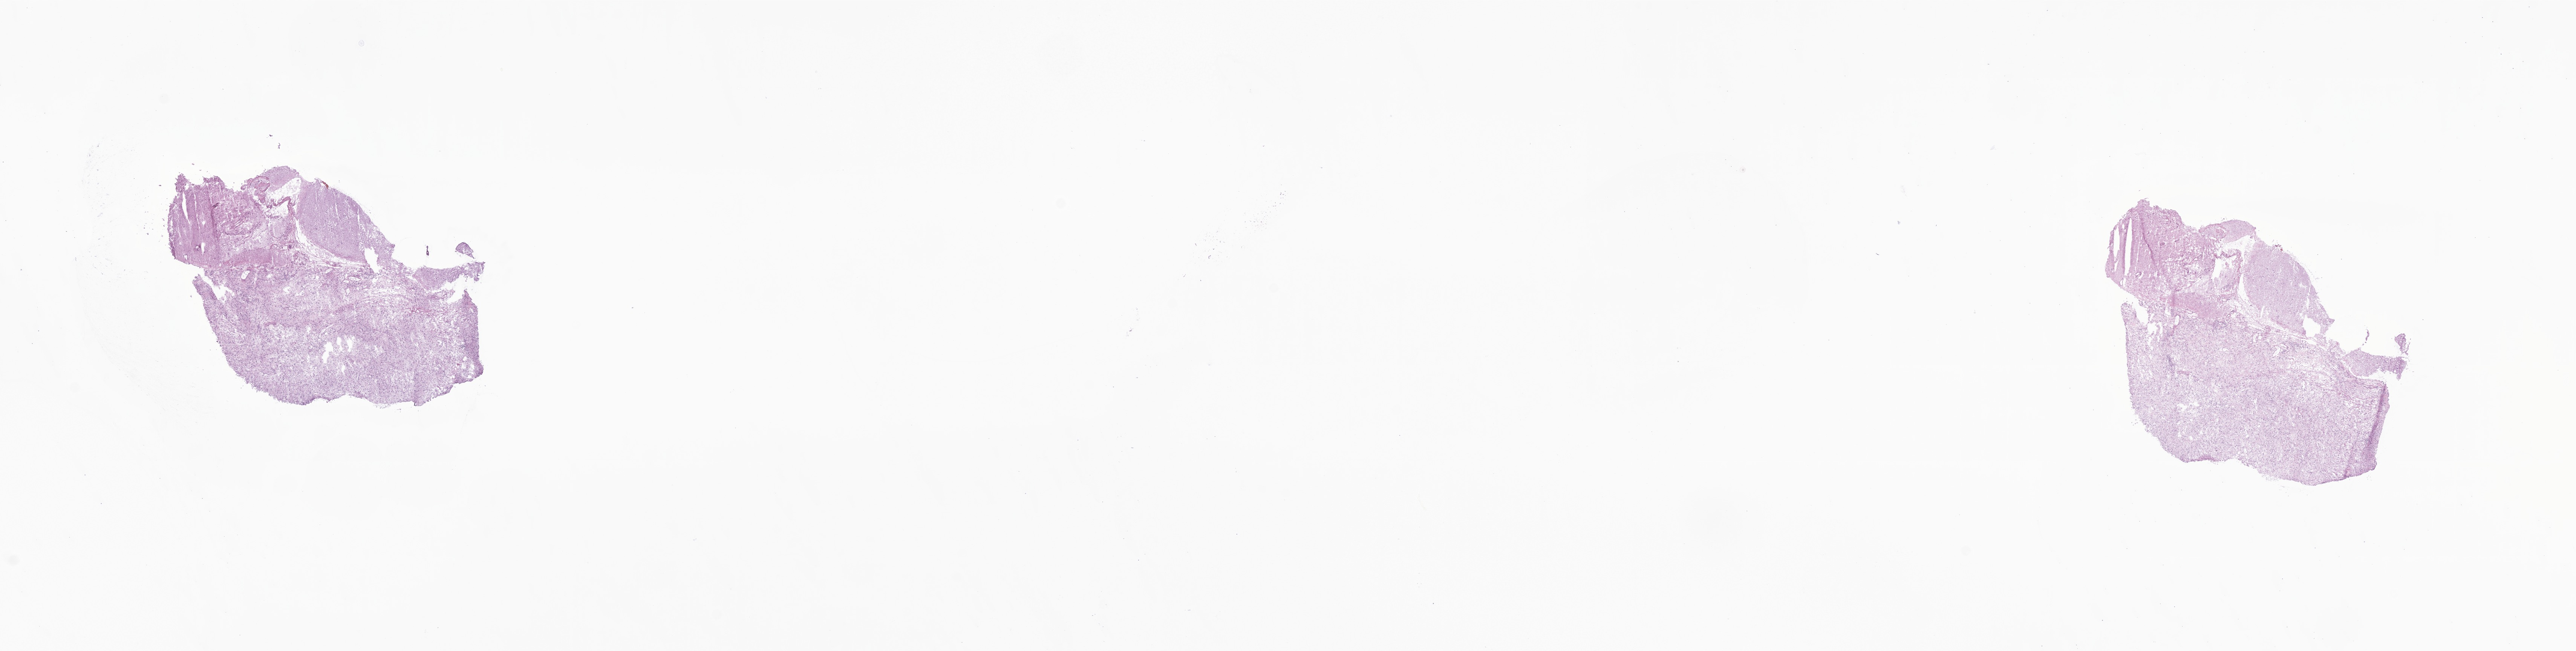
Digitized H&E-stained section of tumor tissue from the occipital lobe, shown as a low-resolution overview of the whole scanned area (about 28.8 x 7.3 mm); frozen section. Male patient, age 168 months.
Diagnosis (ICD-O-3 morphology term): Ganglioglioma, NOS.